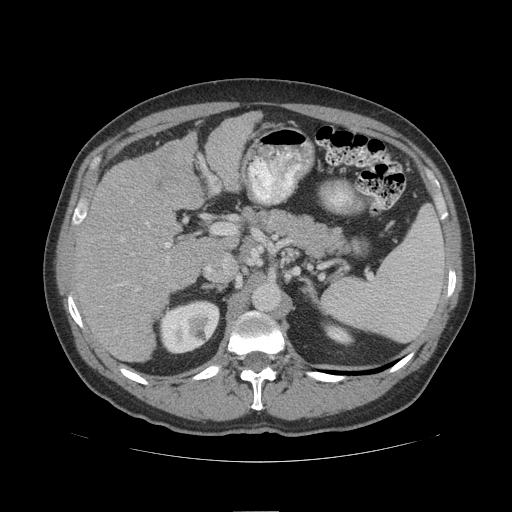
Contrast-enhanced abdominal CT (liver protocol), one axial slice; slice 63 of 109 in the series (ordered by position); reconstruction kernel STANDARD; soft-tissue window (W 400 / L 40 HU); 2.5 mm slice thickness; 512 × 512 image matrix. Case-level facts recorded for this patient, not image findings: diagnosis: hepatocellular carcinoma (patient treated with transarterial chemoembolisation; whether this scan precedes or follows treatment is not stated here); TNM stage (as recorded): Stage-IIIB.
Annotated regions visible in this slice (semi-automatic segmentation, software-assisted and operator-edited):
- liver parenchyma outside the tumour (the mass and vessels are separate outlines, so this box may not span the whole liver): box from (x=74, y=110) to (x=262, y=362) px
- liver vessels: (x=165, y=242)–(x=170, y=247)